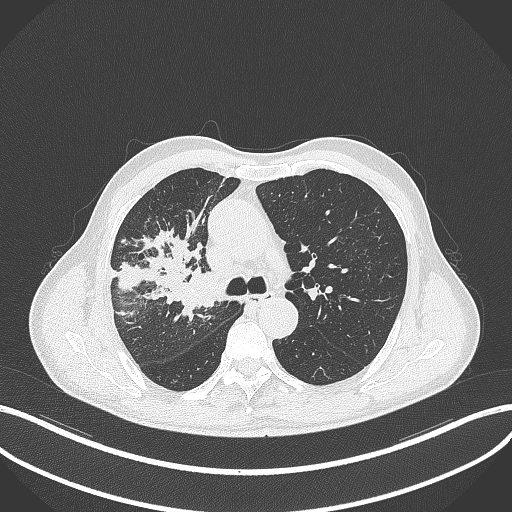
Chest CT, one axial slice. Slice 325 of 490 in the series (ordered by position). 120 kVp. Lung window (W 1500 / L -600 HU). 1 mm slice thickness. 512 × 512 image matrix. Male patient, age 69 years. Case-level facts recorded for this patient, not image findings: clinical TNM (as recorded): T2a N0 M0.
Annotated regions visible in this slice (rectangle marked by the reading radiologist):
- lung tumour (recorded histology: adenocarcinoma): bounding box (x1, y1, x2, y2) in pixels: (176, 263, 222, 318)